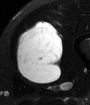
MRI of an extremity soft-tissue mass, one axial slice. Position 25 of 65 along the scan axis. T2-weighted fat-saturated. MR volume resampled by the dataset authors to the PET/CT grid (not the native acquisition matrix). 3.27 mm slice thickness. 90 × 105 image matrix, field of view 88 × 103 mm. Male patient. From the clinical record (not read from this slice): histological type: mixoid liposarcoma; grade: low; site of the primary tumour: left thigh.
Annotated regions visible in this slice (expert contour drawn on MRI and transferred to this co-registered scan by the dataset authors):
- gross tumour volume (mass): bounding box [x1, y1, x2, y2] px = [16, 21, 63, 83]